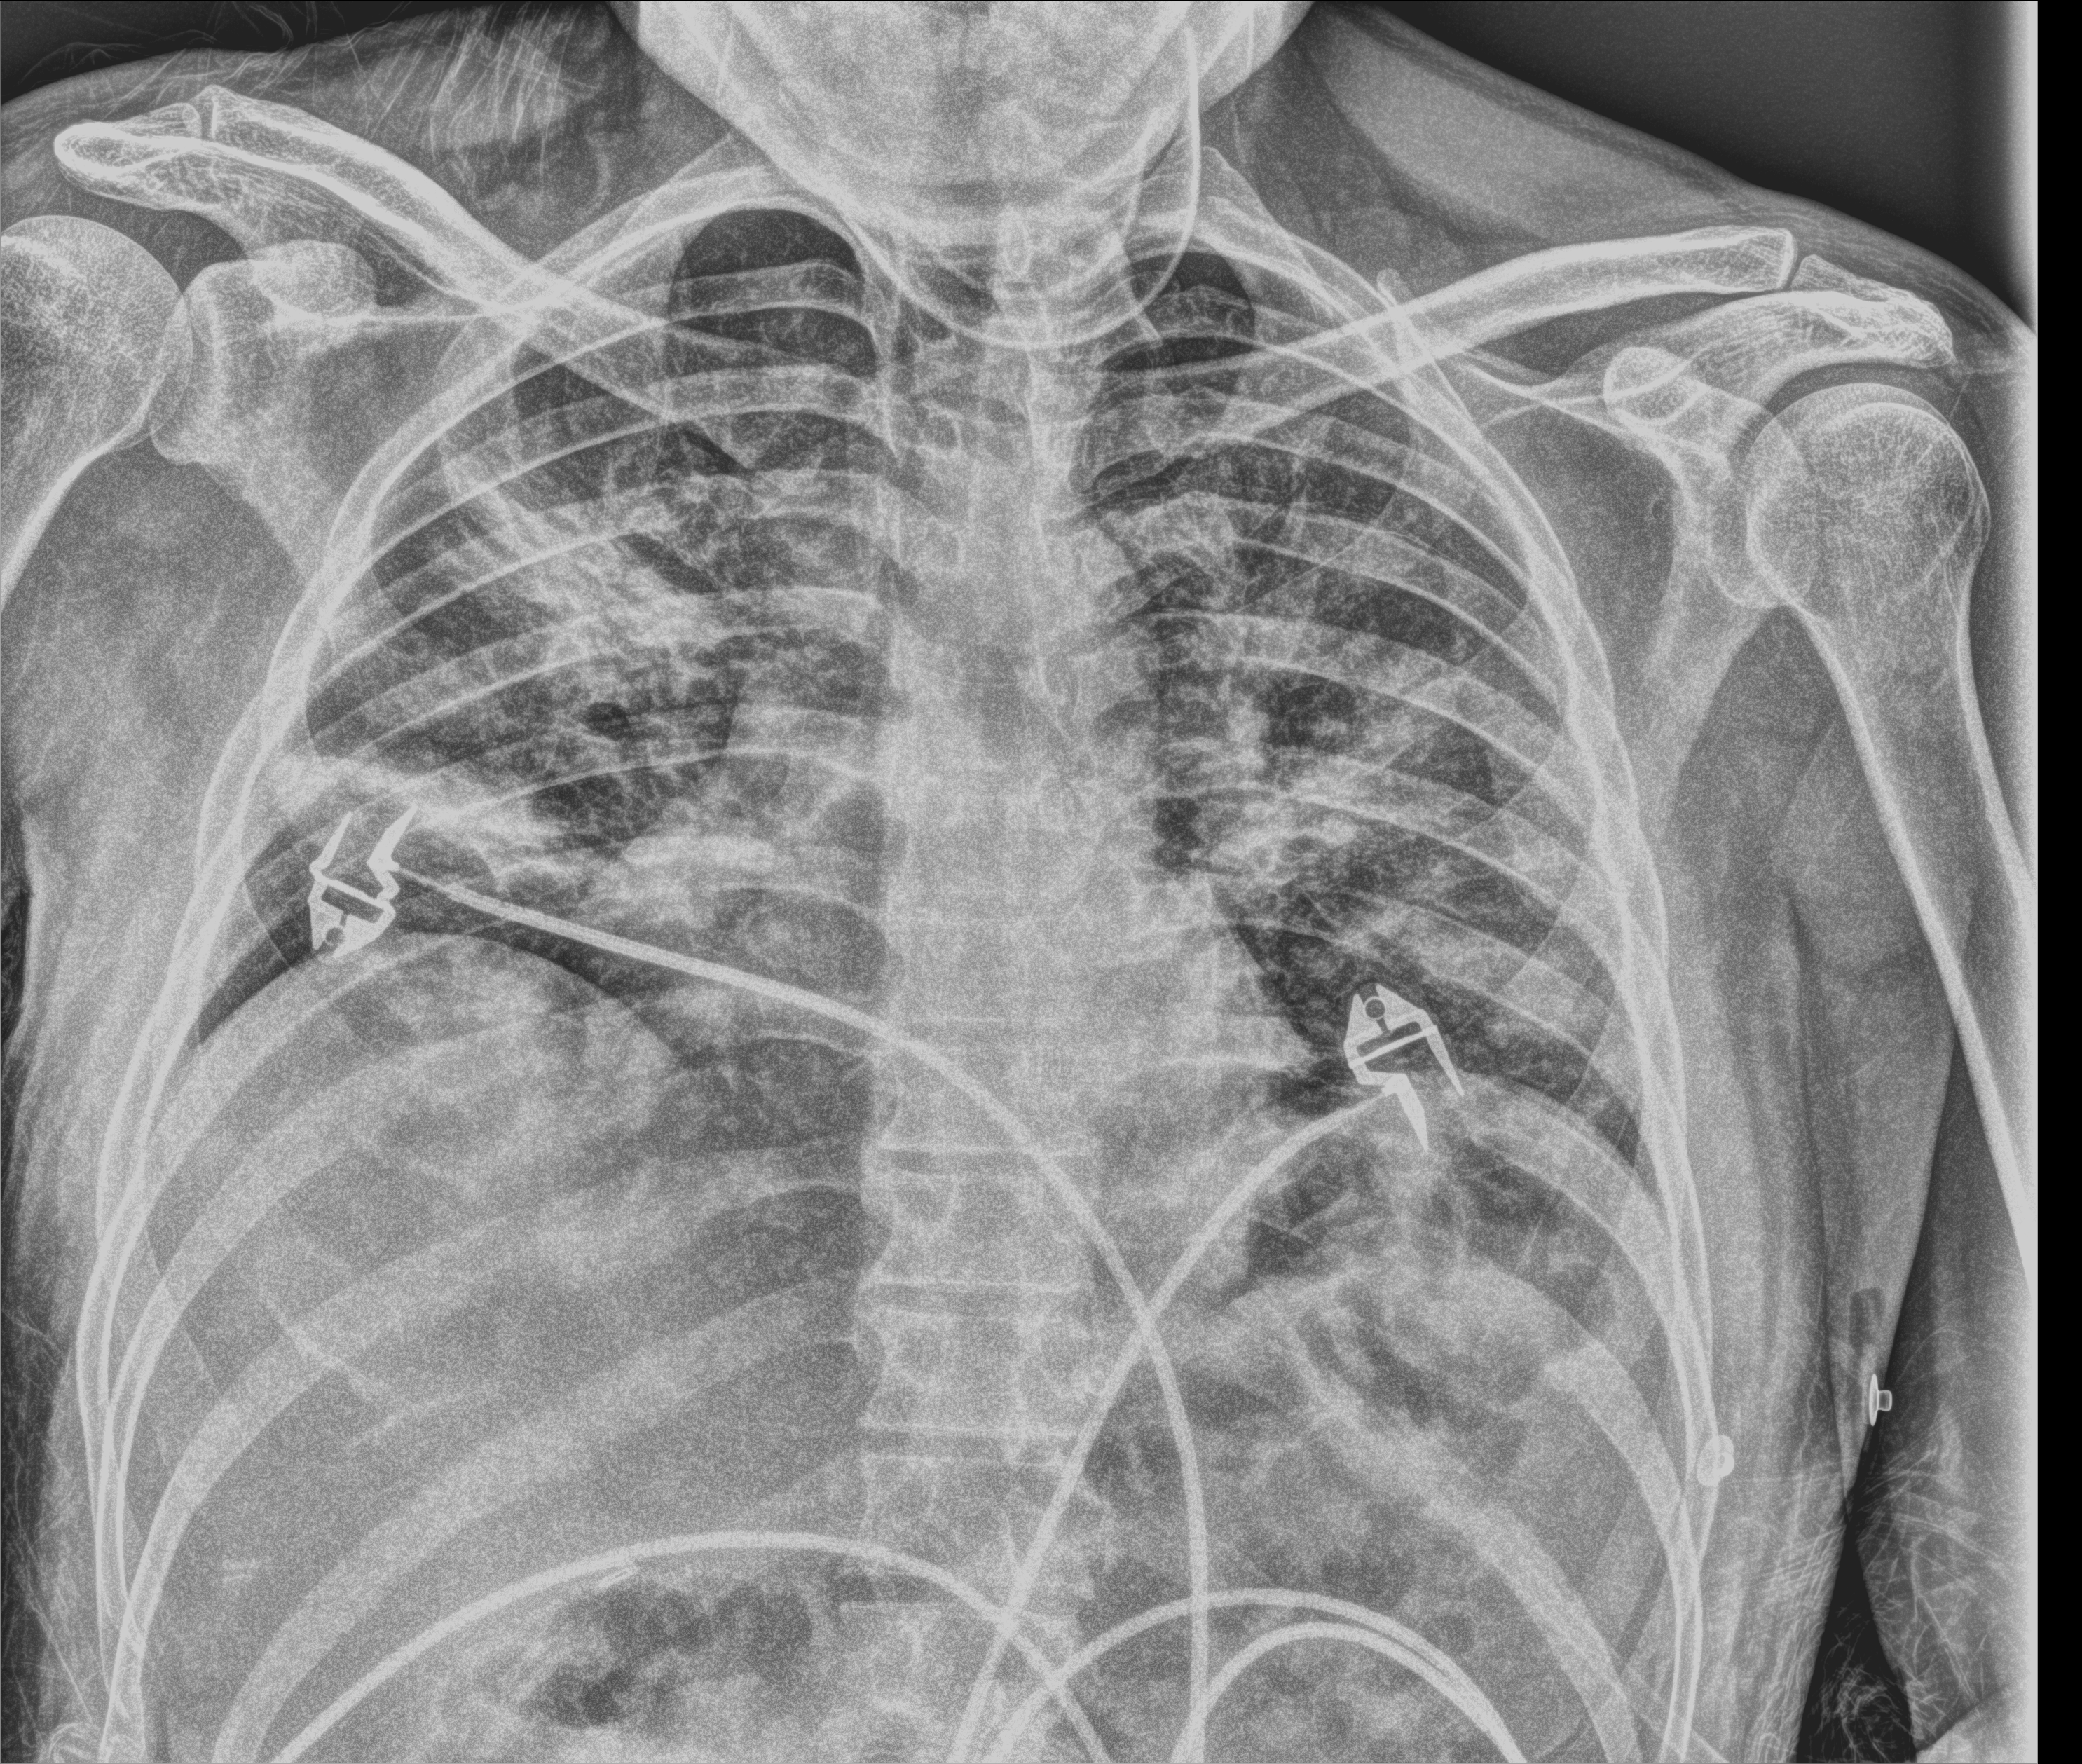
Portable chest radiograph; anteroposterior (AP) projection. Male patient hospitalised with COVID-19, age 18–59 years.
From the hospital-stay record, not from the radiograph (when in the stay this image was taken is not recorded): hypertension (admission record): no; admitted to intensive care during this hospital stay: yes; COPD (admission record): no.